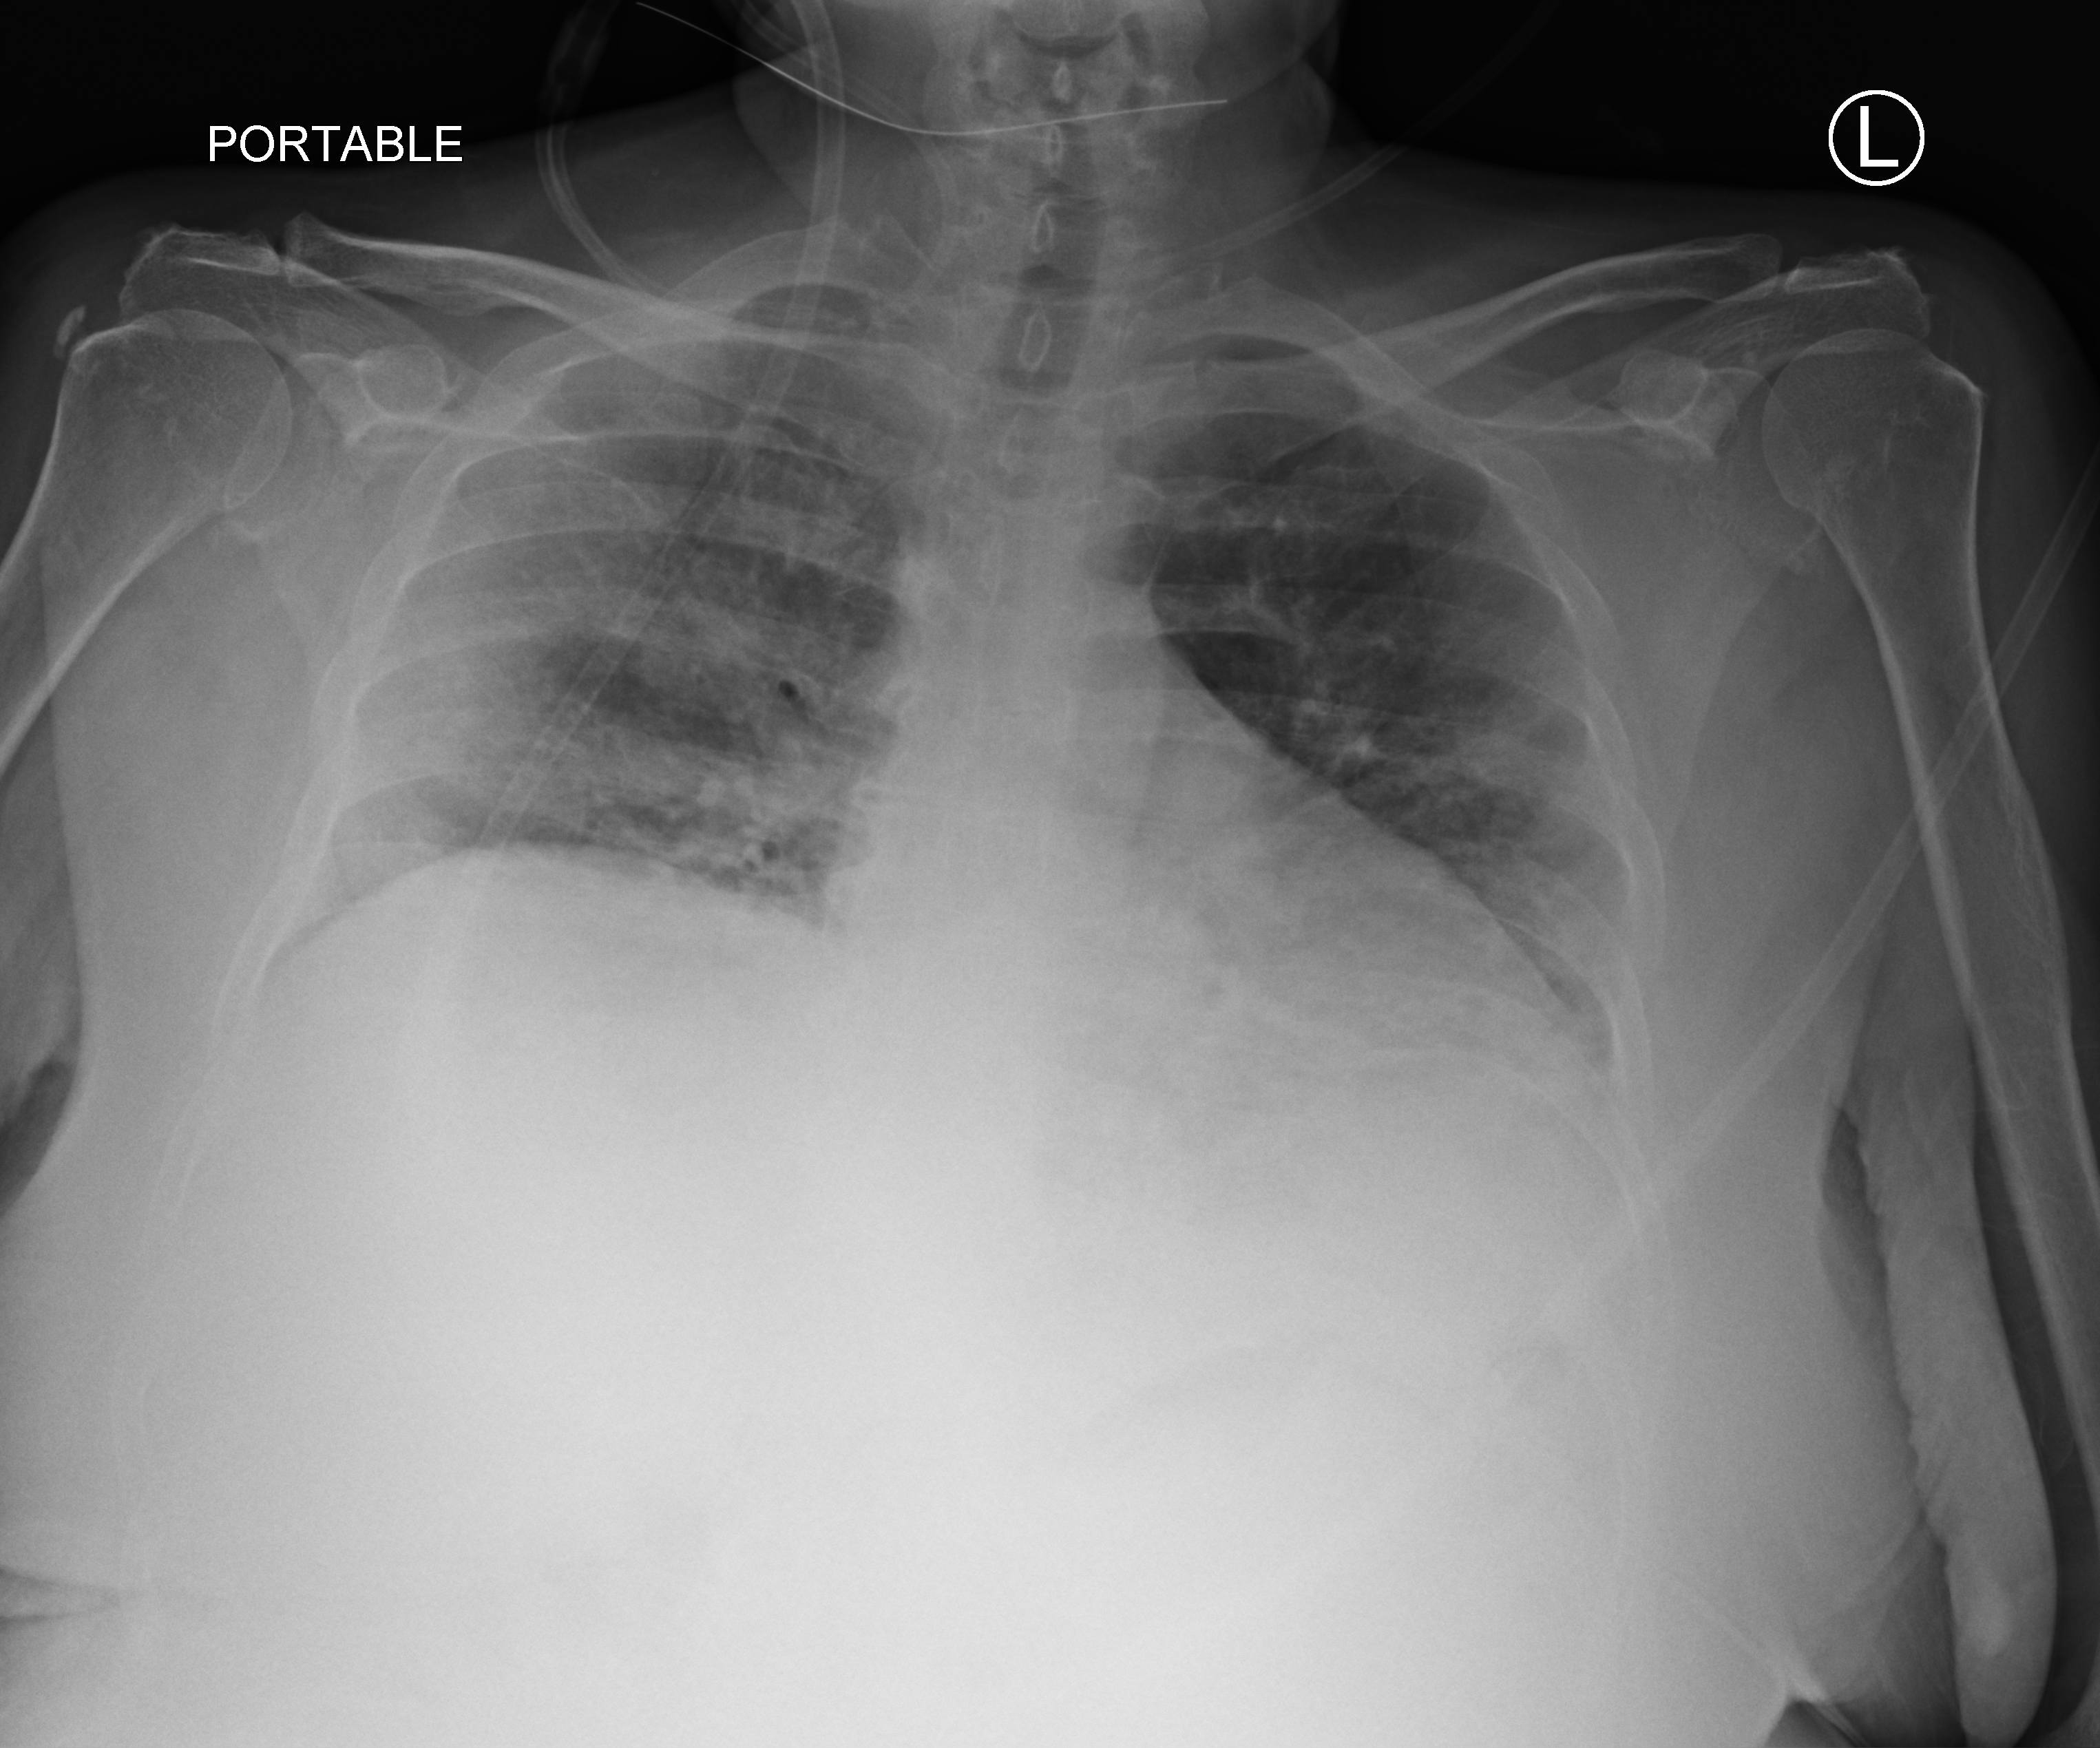
Bedside chest radiograph (computed radiography), anteroposterior (AP) projection. Female patient hospitalised with COVID-19, age 18–59 years.
From the hospital-stay record, not from the radiograph (when in the stay this image was taken is not recorded):
- diabetes (admission record): yes